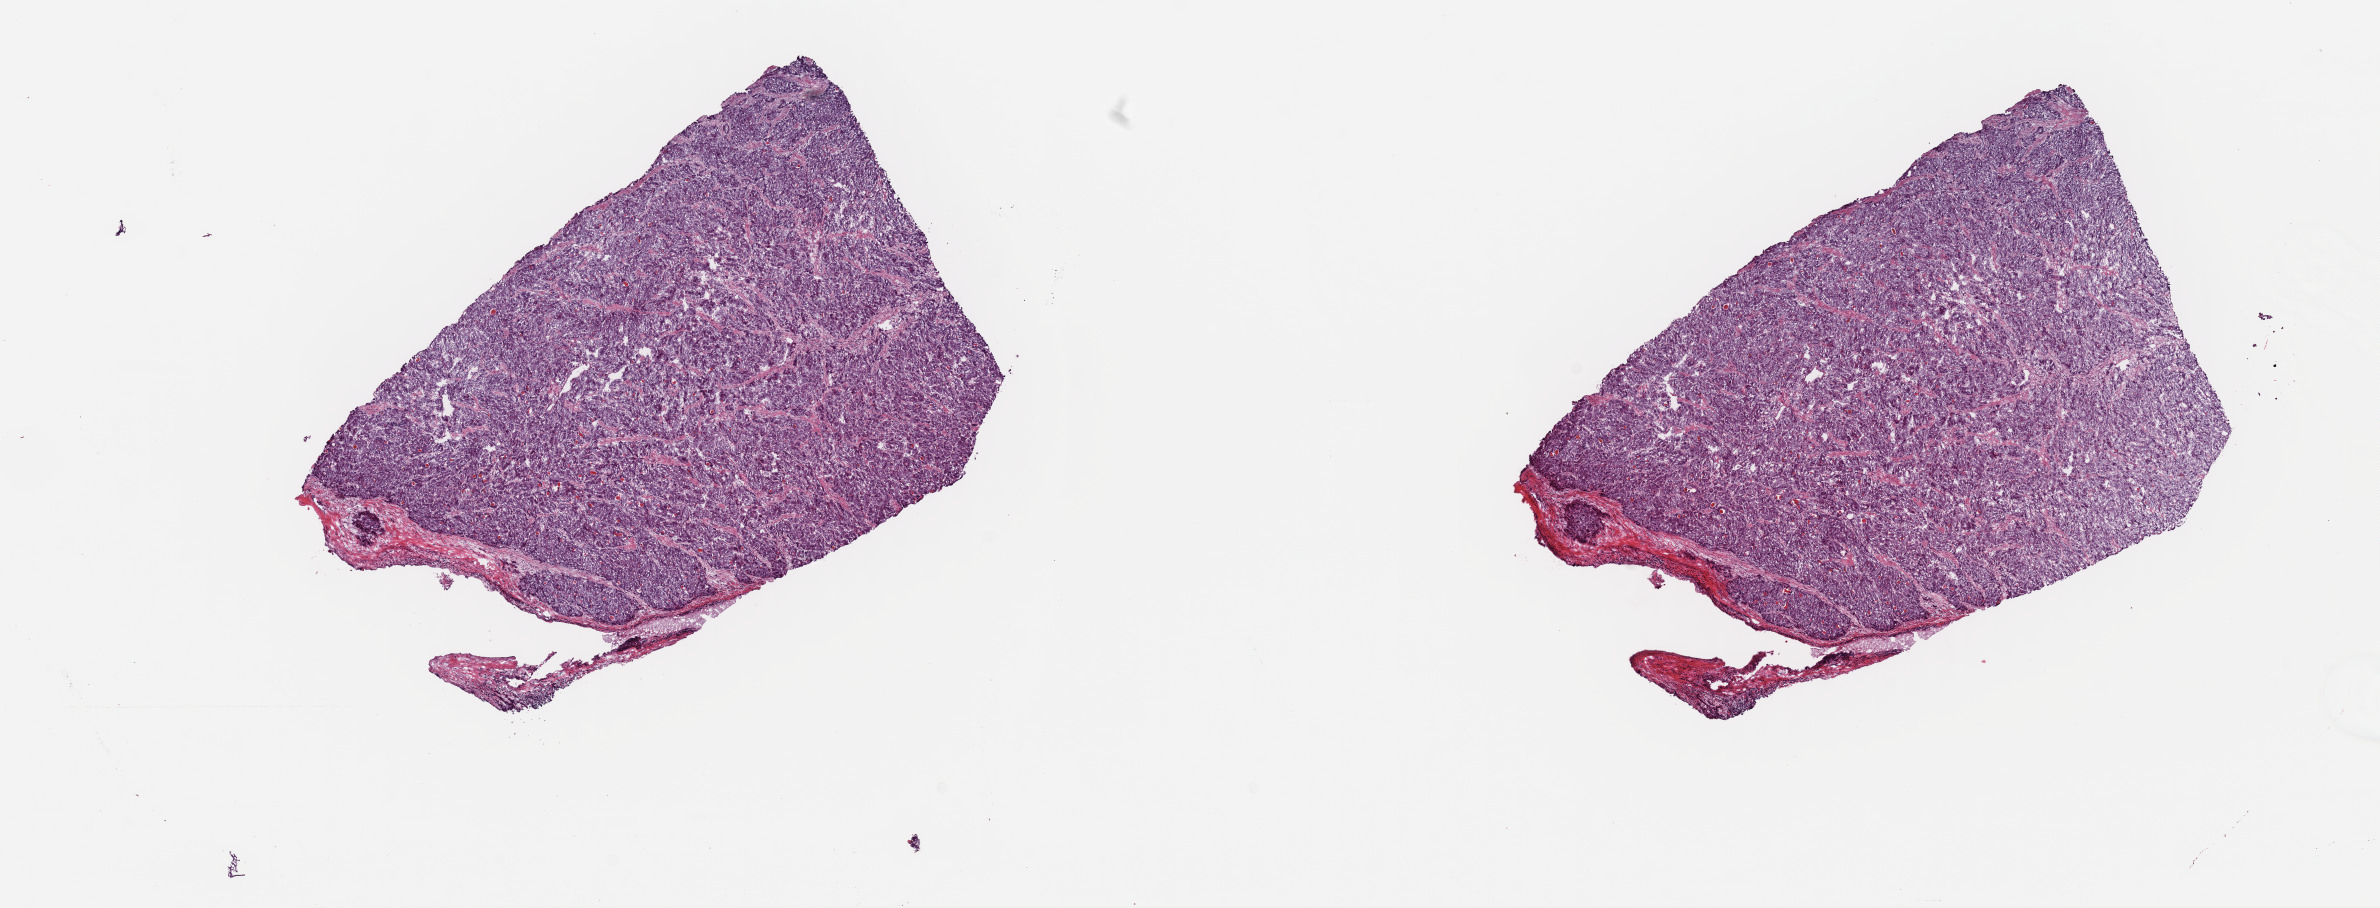
Digitized H&E-stained tissue section (whole slide) — shown as a low-resolution overview of the whole scanned area (about 18.8 x 7.2 mm, slide scanned at 40x); frozen section from the top of the tissue portion; sample: primary tumour, liver. Female, age 78 years at initial diagnosis. Histologic grade: G2 (moderately differentiated). Composition of this section per pathologist review: tumour cells 90%, tumour nuclei 90%, normal cells 0%, stromal cells 10%, necrosis 0%. Infiltration values recorded for this section: lymphocyte infiltration 2%, monocyte infiltration 1%, neutrophil infiltration 0%.
Diagnosis: Hepatocellular carcinoma, NOS. AJCC pathologic stage: I (5th edition). TNM: T1 NX M0.